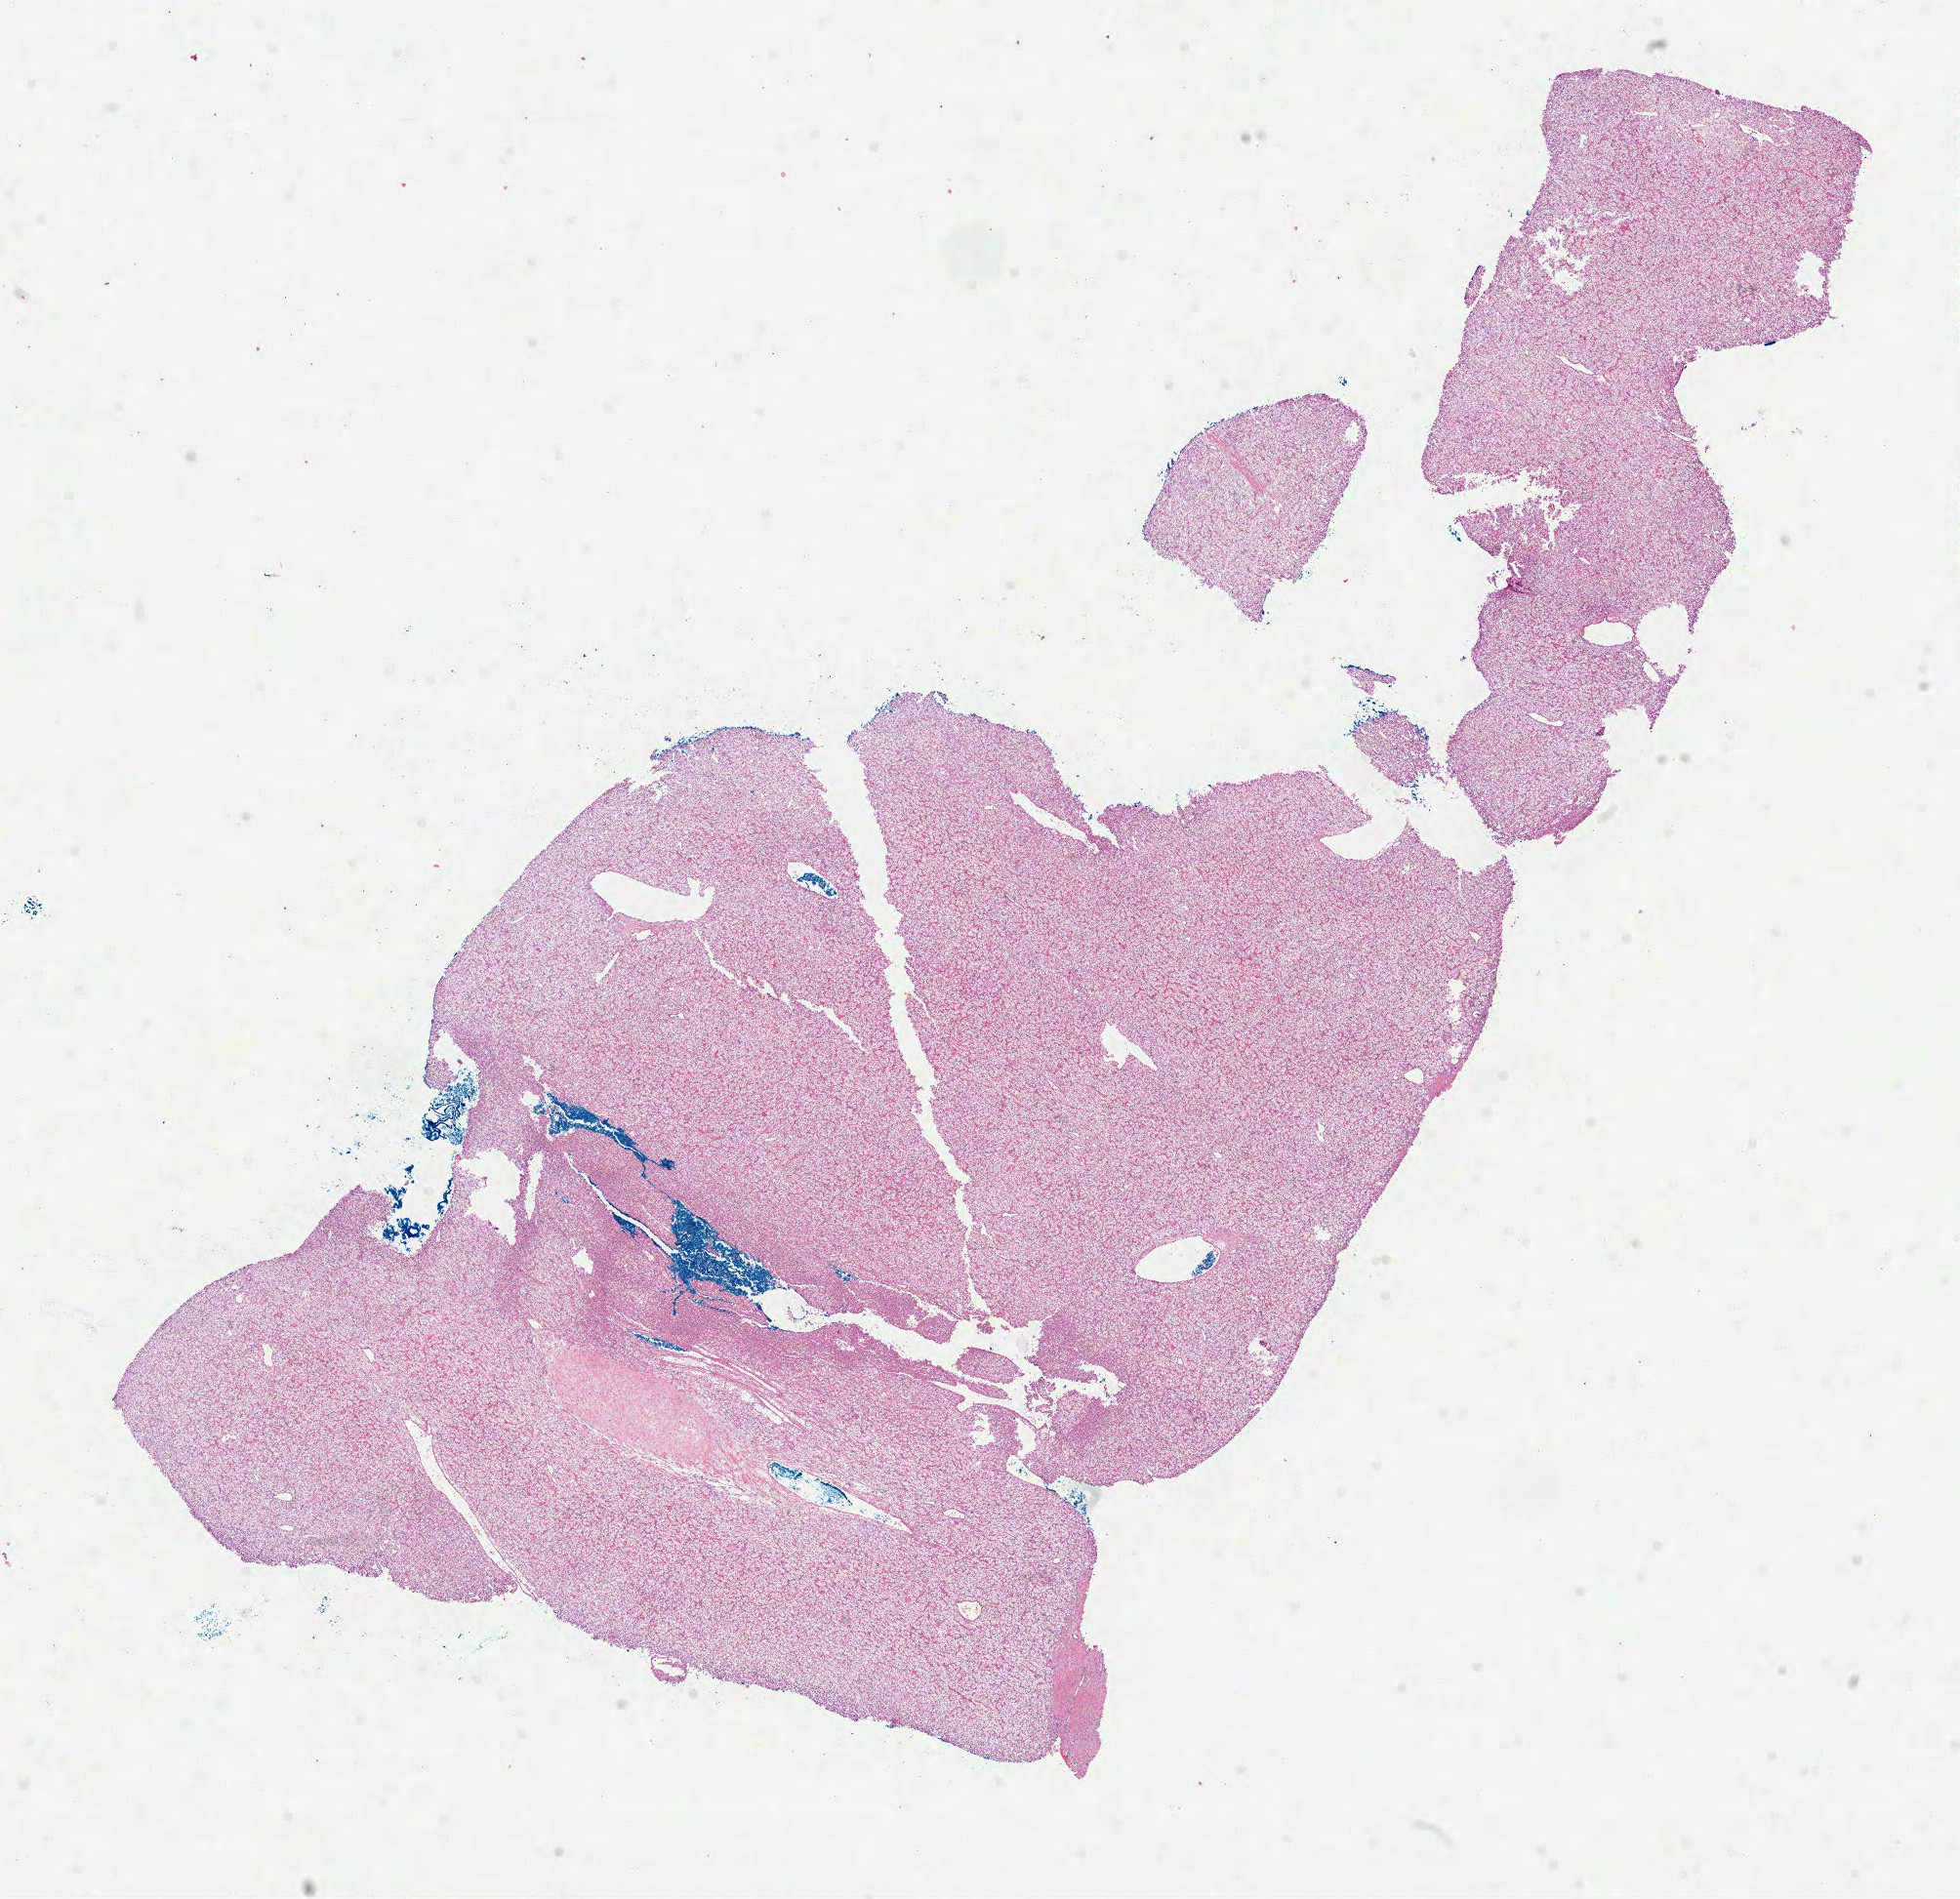
Whole-slide histology image, H&E — low-resolution overview of the scanned area, about 16.2 x 15.7 mm, formalin-fixed paraffin-embedded (FFPE) diagnostic section, sample: primary tumour, kidney. Male patient; age at initial diagnosis 52 years. Histologic grade: G2 (moderately differentiated).
• AJCC pathologic stage: I
• diagnosis: Clear cell adenocarcinoma, NOS